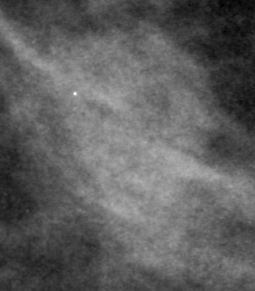
Crop from a digitized film mammogram around one marked abnormality, right breast, CC view.
Marked abnormality: mass, shape focal asymmetric density, margins ill defined; BI-RADS assessment category 4; pathology result (as recorded, not read from the image): benign.